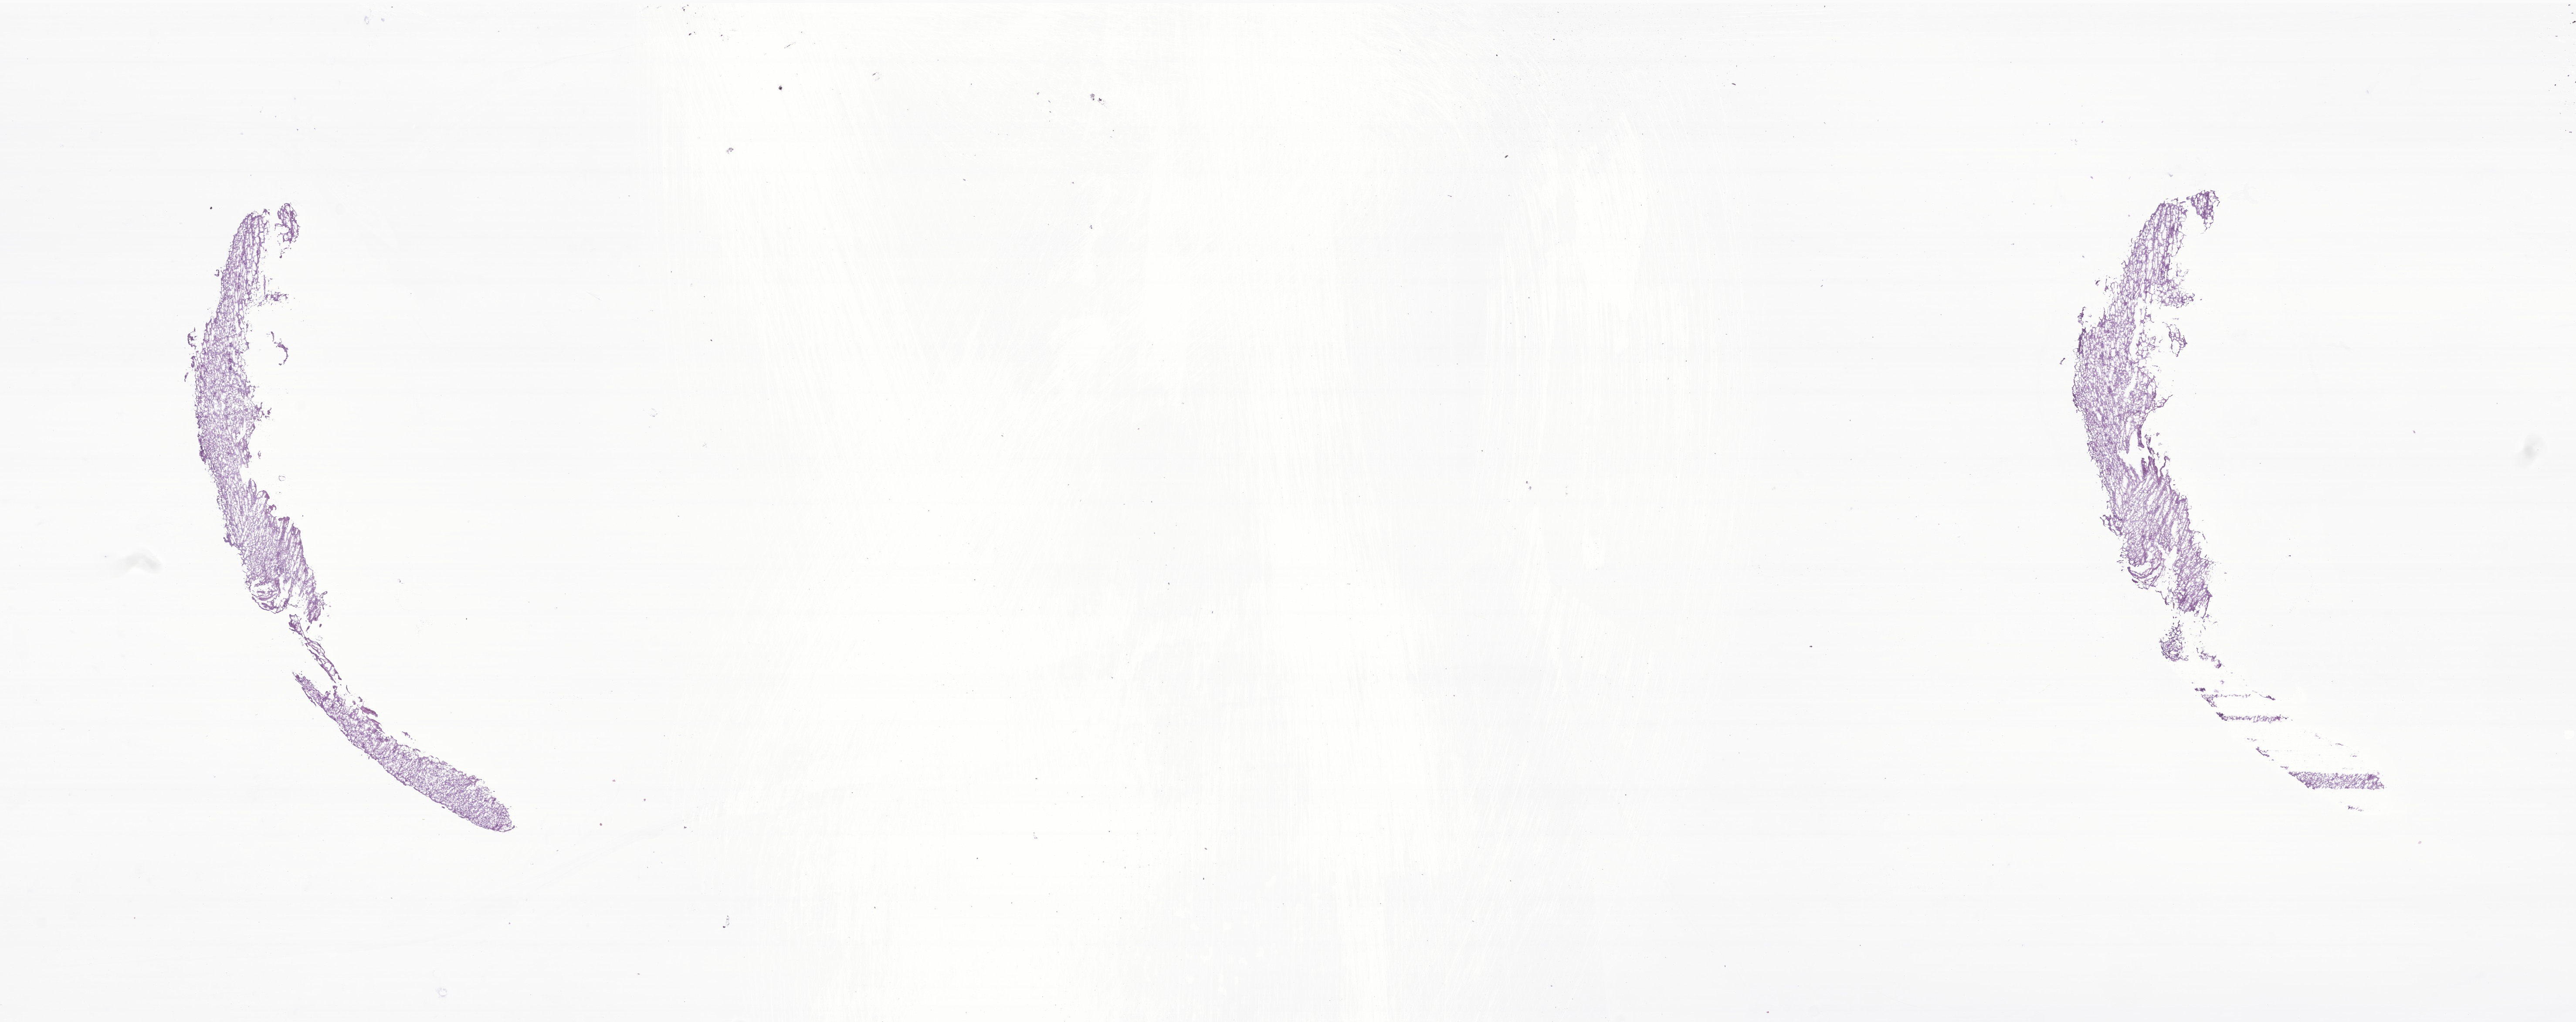
H&E whole-slide image of tumor tissue from the brain, a low-resolution overview of the entire scanned area, about 24.9 x 9.9 mm, cryosection (OCT / tissue freezing medium). Male patient, age 75 months (6 years 3 months).
• diagnosis (ICD-O-3 morphology term): Astrocytoma, NOS